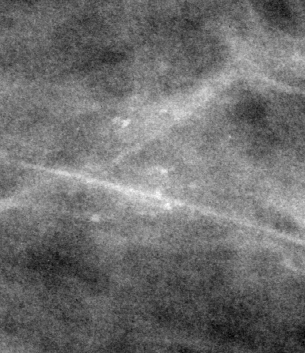
Cropped region of a digitized screen-film mammogram centred on a radiologist-marked abnormality; left breast; MLO view; BI-RADS breast density category 1 (scale 1–4).
Calcifications, morphology pleomorphic, distribution clustered; BI-RADS assessment category 4; pathology (as recorded): benign.